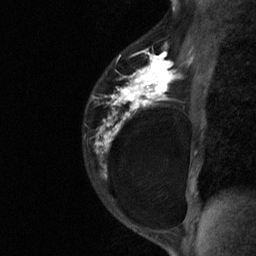
Breast MRI (dynamic contrast-enhanced), one sagittal slice. Position 46 of 64 along the scan axis. Dynamic contrast-enhanced study with each time point stored as its own series, time point 2 of 3 at this slice position (early post-contrast, ordered by acquisition time). 1.5 T. TE 4.8 ms, TR 27 ms. 256 × 256 image matrix, field of view 180 × 180 mm. Patient: female, 34 years. Case-level facts recorded for this patient, not image findings: setting: breast cancer imaged before/during neoadjuvant chemotherapy; receptor status: HR-positive, HER2-negative.
Structures marked on this image (semi-automatically segmented with operator editing):
- analysis volume of interest (the breast-tissue region the enhancement analysis was run in; not a lesion): bounding box <83,44,181,191> (left, top, right, bottom; pixels)
- tumour enhancement mask (voxels above the 90 % enhancement threshold inside the analysis volume of interest): <96,44,180,153>